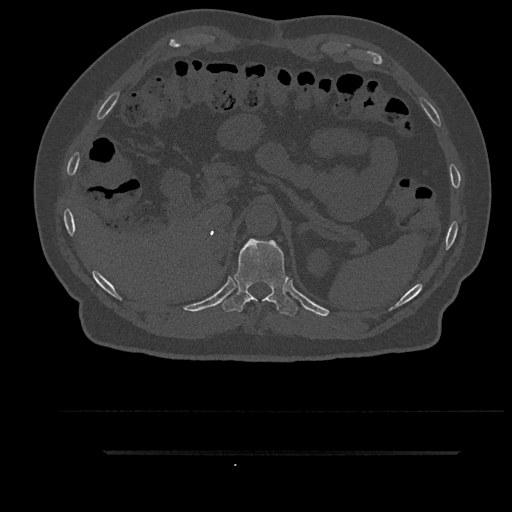
CT including the spine, one axial slice. Position 313 of 797 along the scan axis. 120 kVp. Bone window (W 1800 / L 400 HU). 512 × 512 image matrix, field of view 432 × 432 mm. Male patient, age 63 years. Case-level facts recorded for this patient, not image findings: primary cancer: renal.
Annotated regions visible in this slice (semi-automatically segmented with operator editing):
- T11 vertebra: box from (x=222, y=239) to (x=298, y=316) px